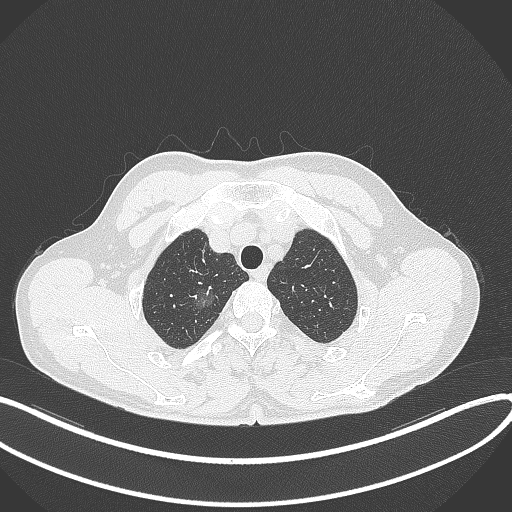
Chest CT, one axial slice; slice 326 of 407 in the series (ordered by position); reconstruction kernel B70f; lung window (W 1500 / L -600 HU); 1 mm slice thickness; 512 × 512 image matrix, field of view 400 × 400 mm. Patient: male, 58 years. Case-level facts recorded for this patient, not image findings: clinical TNM (as recorded): T1c N0 M0; histopathological grade: G1-2.
Structures marked on this image (bounding box drawn by a radiologist):
- lung tumour (recorded histology: adenocarcinoma): box from (x=189, y=278) to (x=219, y=318) px